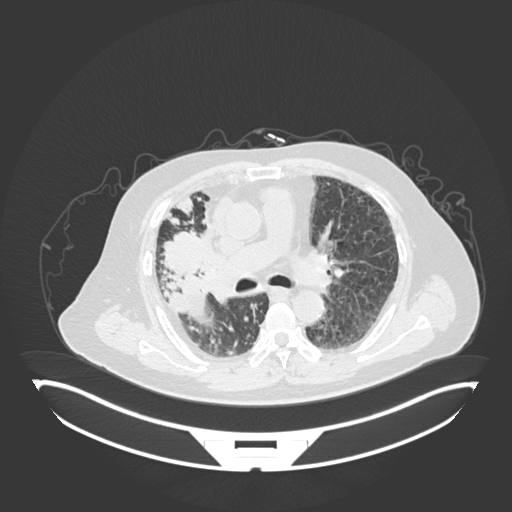
Chest CT, one axial slice. Slice 100 of 201 in the series (ordered by position). Lung window (W 1500 / L -600 HU). 1 mm slice thickness. 512 × 512 image matrix, field of view 500 × 500 mm. Male patient, age 69 years. Case-level facts recorded for this patient, not image findings: clinical TNM (as recorded): T4 N3 M1.
Annotated regions visible in this slice (bounding box drawn by a radiologist):
- lung tumour (recorded histology: adenocarcinoma): box from (x=151, y=227) to (x=212, y=279) px